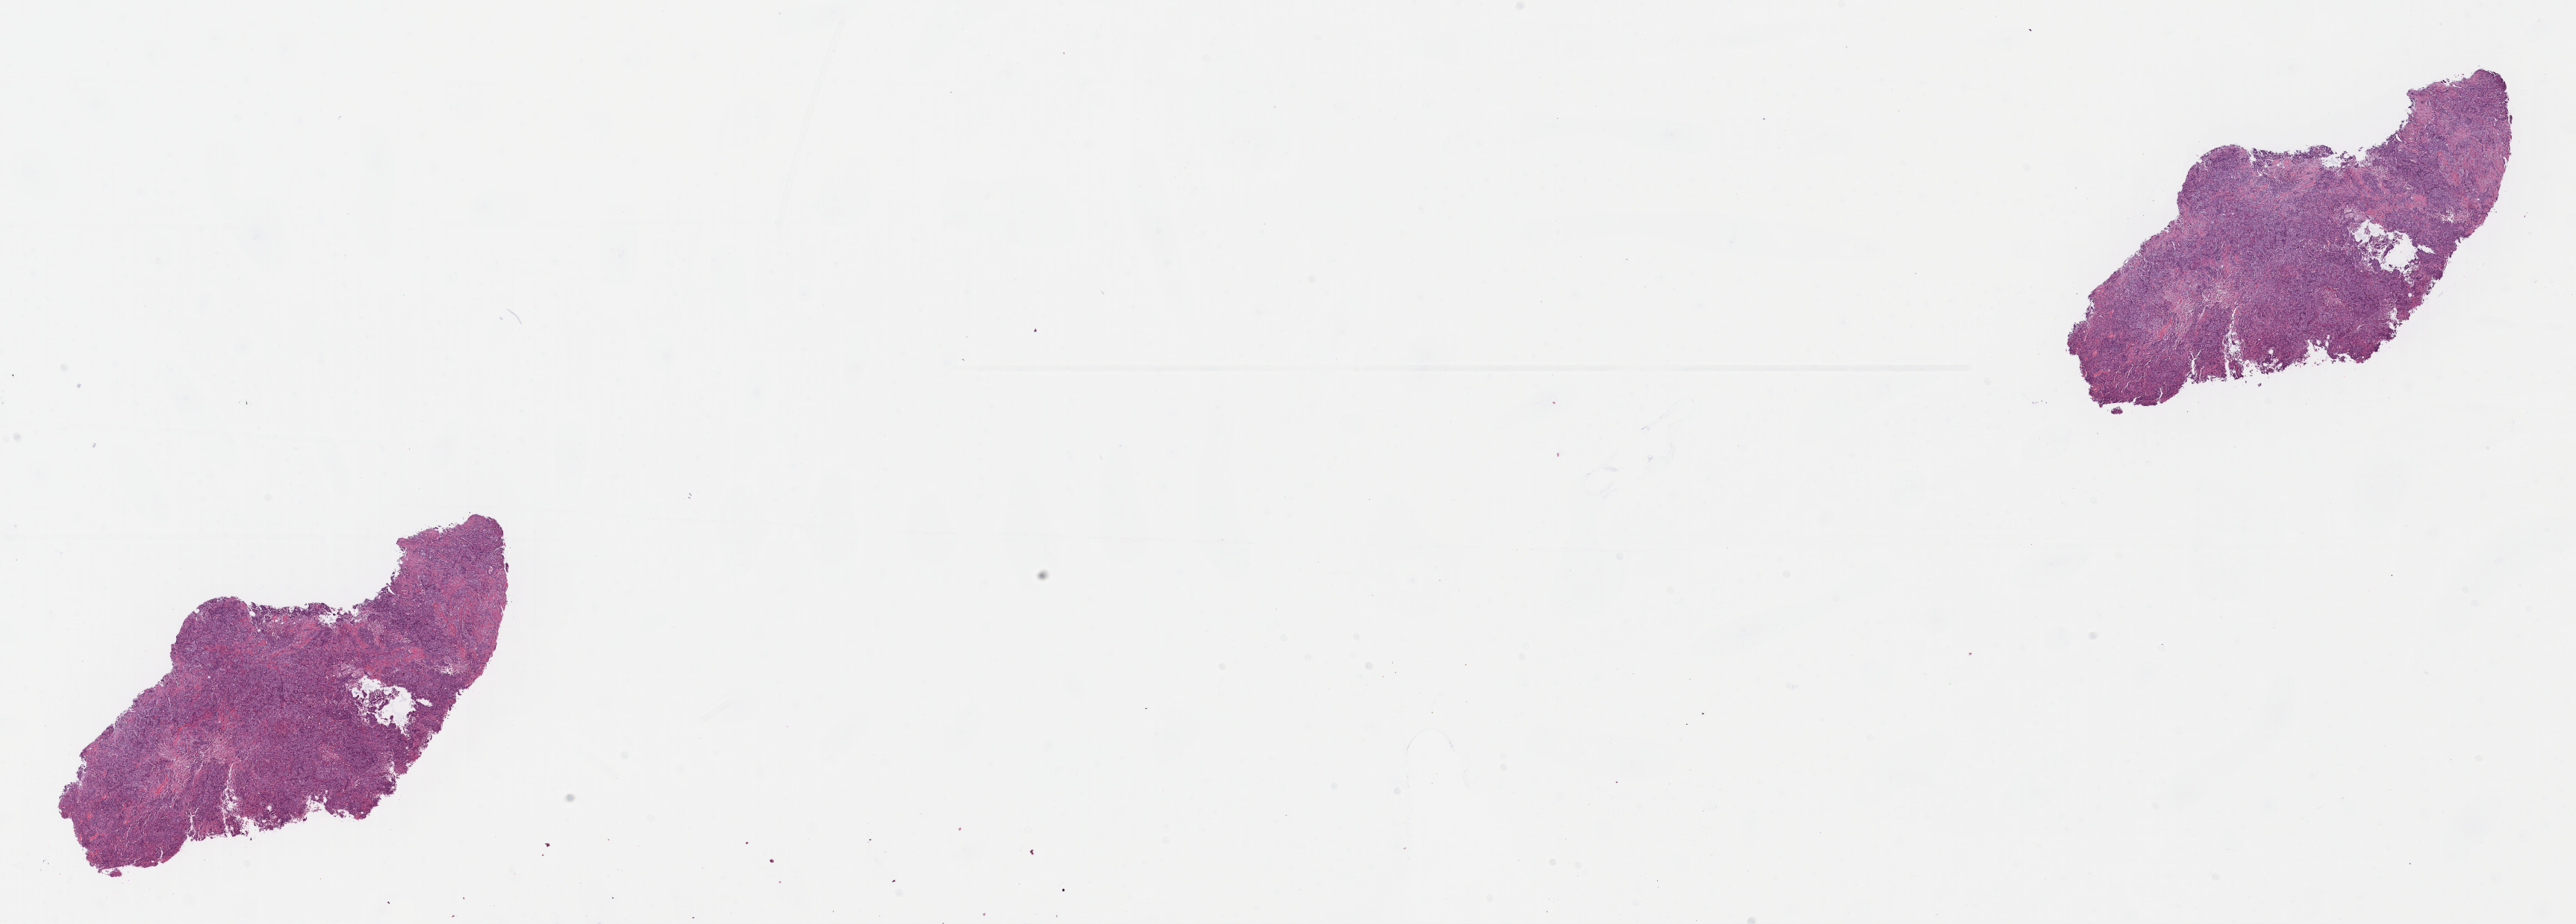
Digitized H&E tissue section (whole slide), low-resolution overview of the scanned area, about 27.1 x 9.7 mm (acquisition: 40x scan), formalin-fixed paraffin-embedded (FFPE) diagnostic section, primary tumour sample from the breast. Patient: female, age at initial diagnosis 48 years.
- AJCC pathologic stage: IIB
- diagnosis: Infiltrating duct carcinoma, NOS
- lymph nodes positive (case pathology): 2 of 14 examined